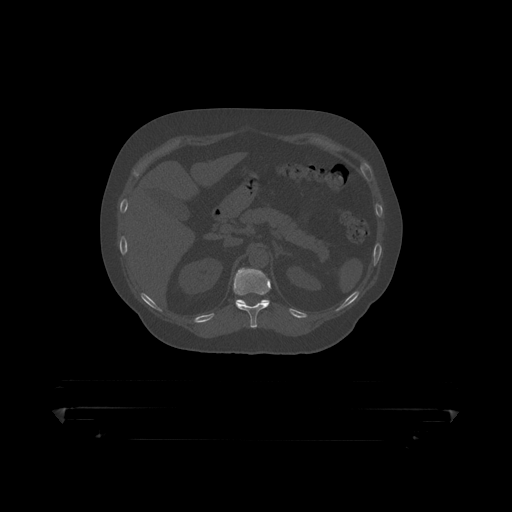
CT including the spine, one axial slice. Slice 188 of 390 in the series (ordered by position). Reconstruction kernel STANDARD. 120 kVp. Bone window (W 1800 / L 400 HU). 1.25 mm slice thickness. 512 × 512 image matrix, field of view 650 × 650 mm. Patient: male, 60 years. Case-level facts recorded for this patient, not image findings: primary cancer: prostate.
Outlined on this slice (semi-automatic segmentation, software-assisted and operator-edited):
- T11 vertebra: bounding box [x1, y1, x2, y2] px = [233, 268, 272, 319]
- T12 vertebra: [236, 299, 270, 304]